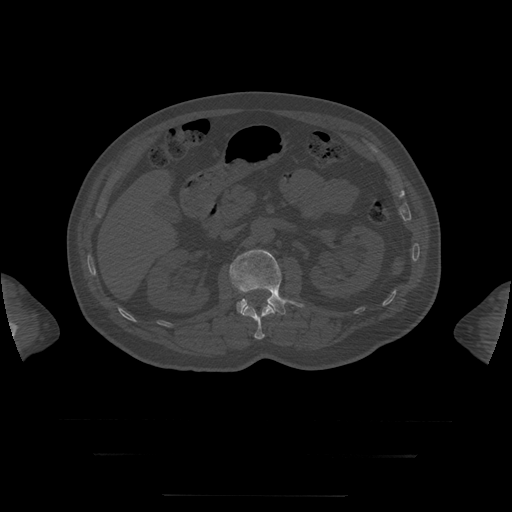
CT including the spine, one axial slice; position 34 of 397 along the scan axis; reconstruction kernel STANDARD; bone window (W 1800 / L 400 HU); 1.25 mm slice thickness; 512 × 512 image matrix. Patient age 73 years. From the clinical record (not read from this slice): primary cancer: prostate.
Annotated regions visible in this slice (semi-automatically segmented with operator editing):
- L1 vertebra: bounding box (x1, y1, x2, y2) in pixels: (242, 303, 275, 340)